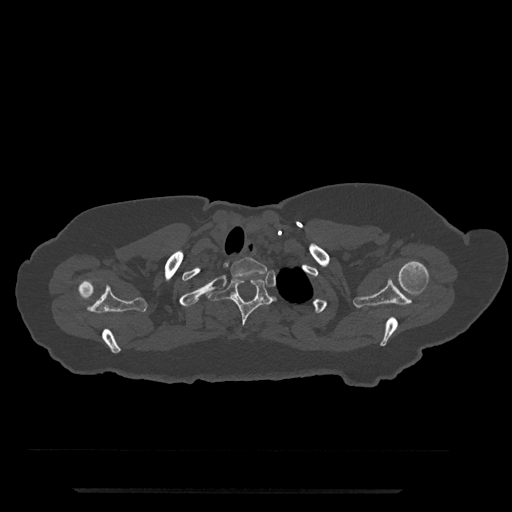
CT including the spine, one axial slice. Position 681 of 797 along the scan axis. Reconstruction kernel Br40s/3. Bone window (W 1800 / L 400 HU). 0.5 mm slice thickness. 512 × 512 image matrix, field of view 440 × 440 mm. Patient: female, 51 years. From the clinical record (not read from this slice): primary cancer: neuro.
Structures marked on this image (semi-automatic segmentation, software-assisted and operator-edited):
- T1 vertebra: bounding box <230,257,267,276> (left, top, right, bottom; pixels)
- T2 vertebra: <207,277,277,326>